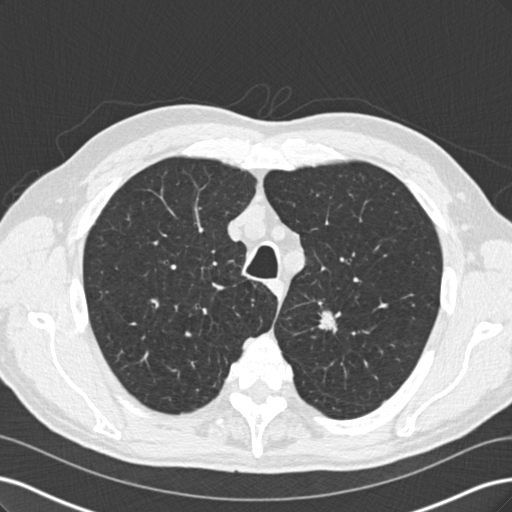
Low-dose screening chest CT, one axial slice; position 176 of 219 along the scan axis; reconstruction kernel B30f; 120 kVp; lung window (W 1500 / L -600 HU); 2 mm slice thickness; 512 × 512 image matrix, field of view 360 × 360 mm.
Structures marked on this image (manually delineated by an expert):
- lesion 1 (tumor, upper lobe of left lung): bounding box <318,310,341,333> (left, top, right, bottom; pixels)